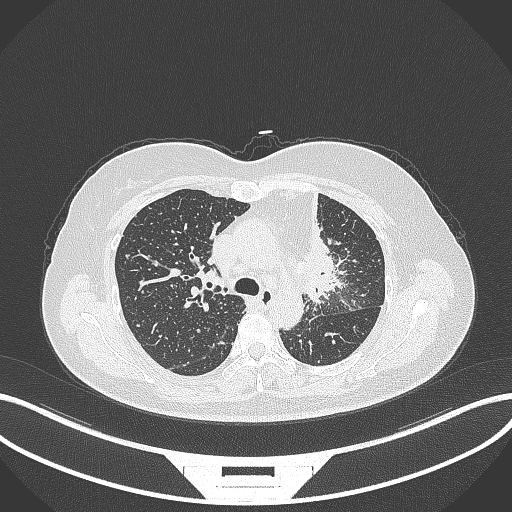
Chest CT, one axial slice. Position 226 of 348 along the scan axis. Reconstruction kernel B70f. Lung window (W 1500 / L -600 HU). 1 mm slice thickness. 512 × 512 image matrix, field of view 400 × 400 mm. Female patient, age 49 years. From the clinical record (not read from this slice): clinical TNM (as recorded): T1c N0 M1.
Structures marked on this image (rectangle marked by the reading radiologist):
- lung tumour (recorded histology: adenocarcinoma): box from (x=293, y=194) to (x=342, y=305) px